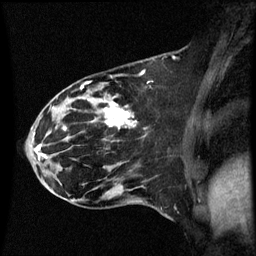
Breast MRI (dynamic contrast-enhanced), one sagittal slice. Slice 23 of 60 in the series (ordered by position). Dynamic contrast-enhanced series, image 2 of 3 at this slice position (ordered by acquisition). 1.5 T. TE 4.2 ms, TR 8.9 ms. 256 × 256 image matrix, field of view 200 × 200 mm. Patient: female, 44 years. Case-level facts recorded for this patient, not image findings: setting: breast cancer imaged before/during neoadjuvant chemotherapy; receptor status: HR-positive, HER2-negative.
Annotated regions visible in this slice (semi-automatic segmentation, software-assisted and operator-edited):
- analysis volume of interest (the breast-tissue region the enhancement analysis was run in; not a lesion): box from (x=43, y=78) to (x=147, y=189) px
- tumour enhancement mask (voxels above the 70 % enhancement threshold inside the analysis volume of interest): (x=64, y=86)–(x=133, y=129)